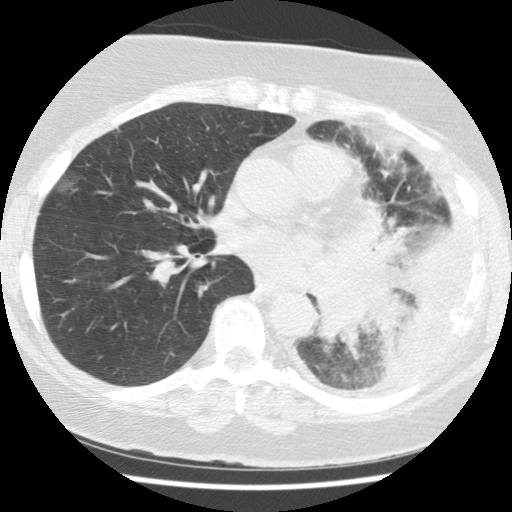
Axial slice from a low-dose chest CT screening exam. Baseline screening round. Lung window (W 1500 / L -600 HU). 2.5 mm slice thickness. Standard (soft-tissue) reconstruction kernel (STANDARD). Female participant, aged 65 years at enrolment. Current smoker at enrolment.
Expert reader's lesion annotation, bounding box [x1, y1, x2, y2] px = [303, 282, 410, 368]. The exam's reader record, not a measurement of the box and not confirmed to be the same lesion: non-calcified nodule or mass ≥4 mm, left lower lobe, 74 × 48 mm, spiculated (stellate) margins, soft tissue attenuation.